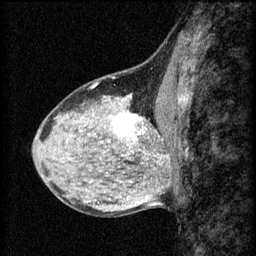
Breast MRI (dynamic contrast-enhanced), one sagittal slice; position 25 of 60 along the scan axis; 3 images stored at this slice position (order not interpretable as contrast timing); 1.5 T; TE 4.2 ms, TR 8.2 ms; 2 mm slice thickness; 256 × 256 image matrix, field of view 180 × 180 mm. Patient: female, 40 years.
Outlined on this slice (semi-automatic segmentation, software-assisted and operator-edited):
- analysis volume of interest (the breast-tissue region the enhancement analysis was run in; not a lesion): box from (x=108, y=108) to (x=167, y=159) px
- tumour enhancement mask (voxels above the 70 % enhancement threshold inside the analysis volume of interest): (x=114, y=114)–(x=145, y=141)